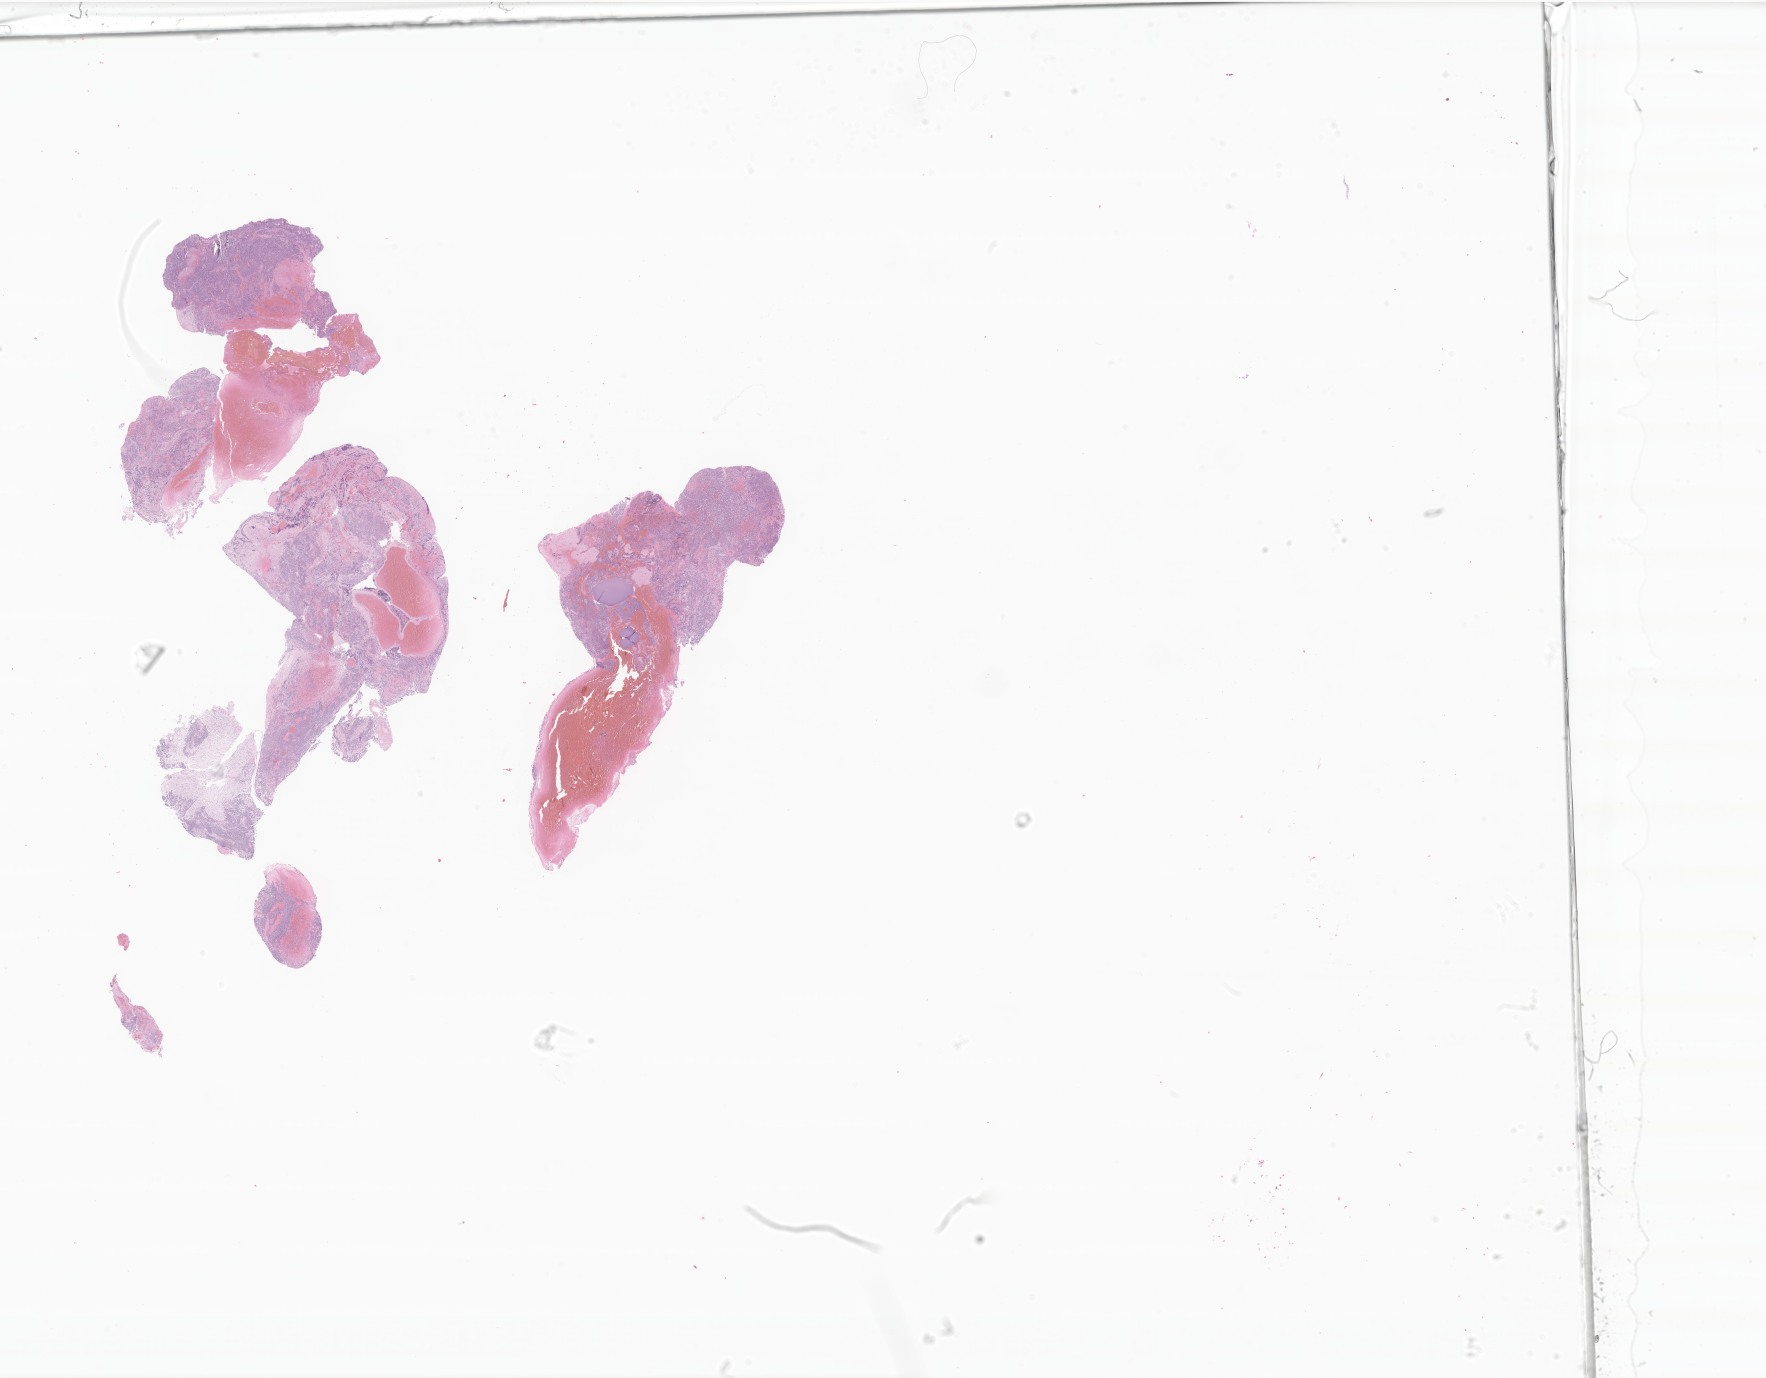
Hematoxylin and eosin (H&E) whole-slide image of tumor tissue from the brain, a low-resolution overview of the entire scanned area, about 29.8 x 23.2 mm; formalin-fixed, paraffin-embedded (FFPE) tissue. Male patient, age 461 days (about 1.3 years).
• recorded diagnosis: Pineoblastoma